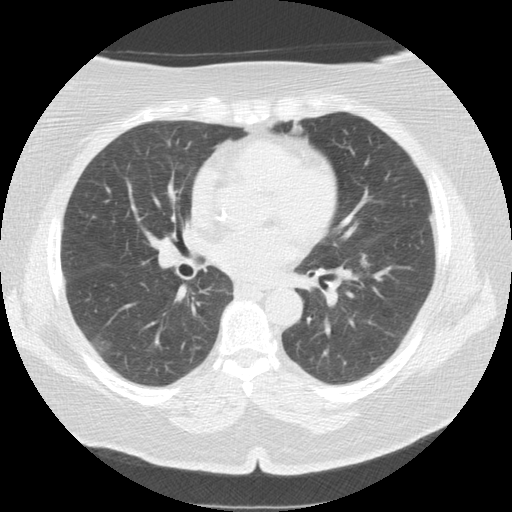
Axial slice from a low-dose chest CT screening exam; first (baseline) screen; lung window (W 1500 / L -600 HU); 2.5 mm slice thickness; slice 76 of 161 in the series. Female, age 65 years at enrolment. Current smoker at enrolment.
Expert-annotated lung lesion, bounding box [x1, y1, x2, y2] px = [349, 246, 378, 275]. No non-calcified nodule or mass ≥4 mm was recorded by the screening reader at this exam. Official screen result: negative screen, minor abnormalities not suspicious for lung cancer. Lung cancer was diagnosed 986 days after this screen (after the third annual screen): adenocarcinoma, NOS, left lower lobe, moderately differentiated (G2), stage IA (AJCC 6th edition), 12 mm at pathology.